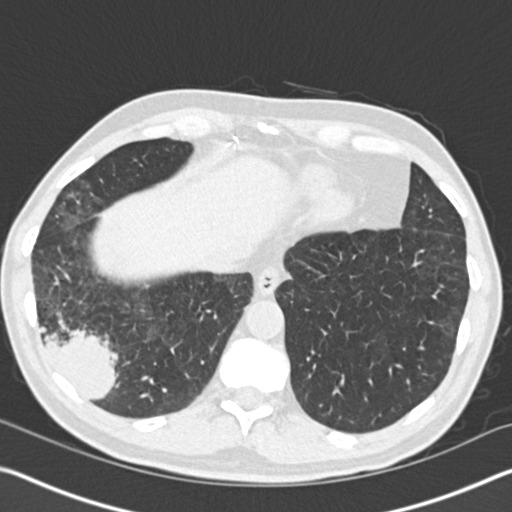
Chest CT (low-dose screening protocol), one axial image. Baseline annual screen. Lung window (W 1500 / L -600 HU). 2 mm slice thickness. 512 × 512 image matrix. Male, age 61 years at enrolment. Current smoker at enrolment.
Expert-annotated lung lesion, bounding box <15,281,140,415> (left, top, right, bottom; pixels). The exam's reader record, not a measurement of the box and not confirmed to be the same lesion: non-calcified nodule or mass ≥4 mm, right lower lobe, 52 × 36 mm, spiculated (stellate) margins, soft tissue attenuation. Official screen result: positive, change unspecified: nodule(s) >= 4 mm or enlarging nodule(s), mass(es), or other non-specific abnormalities suspicious for lung cancer.